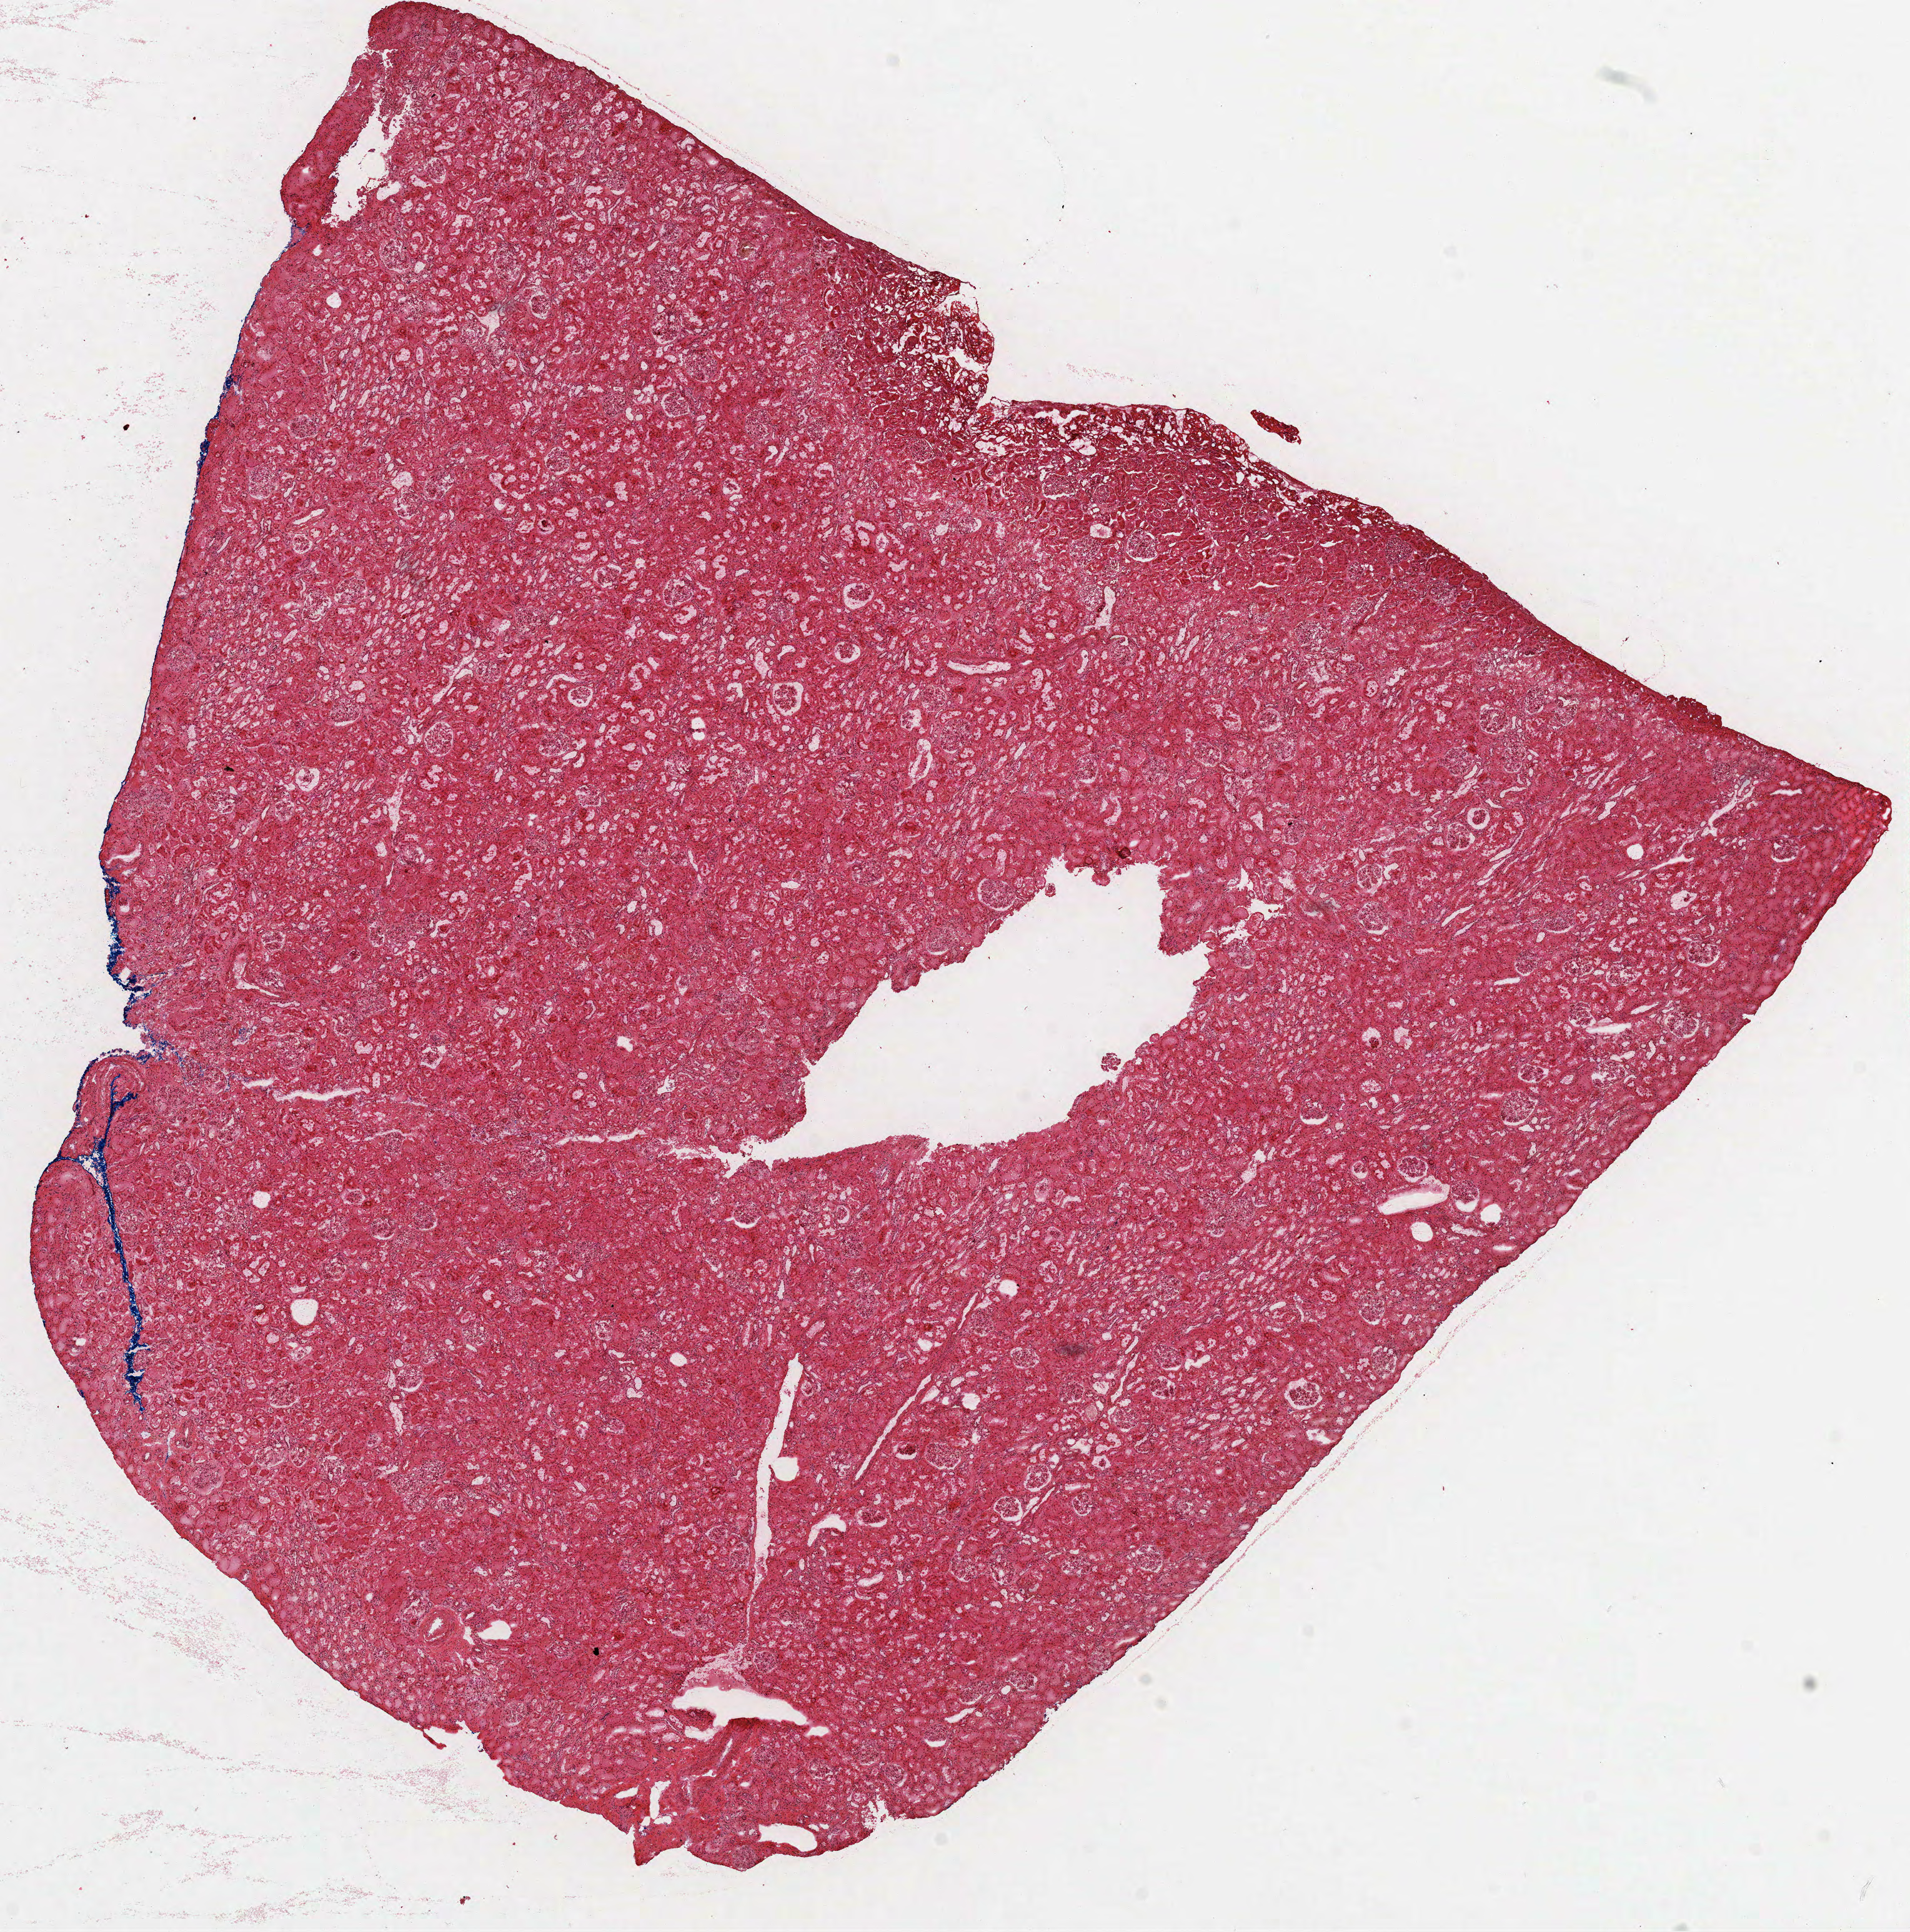
Whole-slide histology image, H&E, low-resolution overview of the scanned area, about 12.3 x 12.5 mm (from a 40x scan); frozen section; kidney, solid tissue normal (non-tumour tissue) sample. Female, age 45 years at initial diagnosis.
This section: solid tissue normal (non-tumour) sample from the same patient. Patient diagnosis: Papillary adenocarcinoma, NOS.